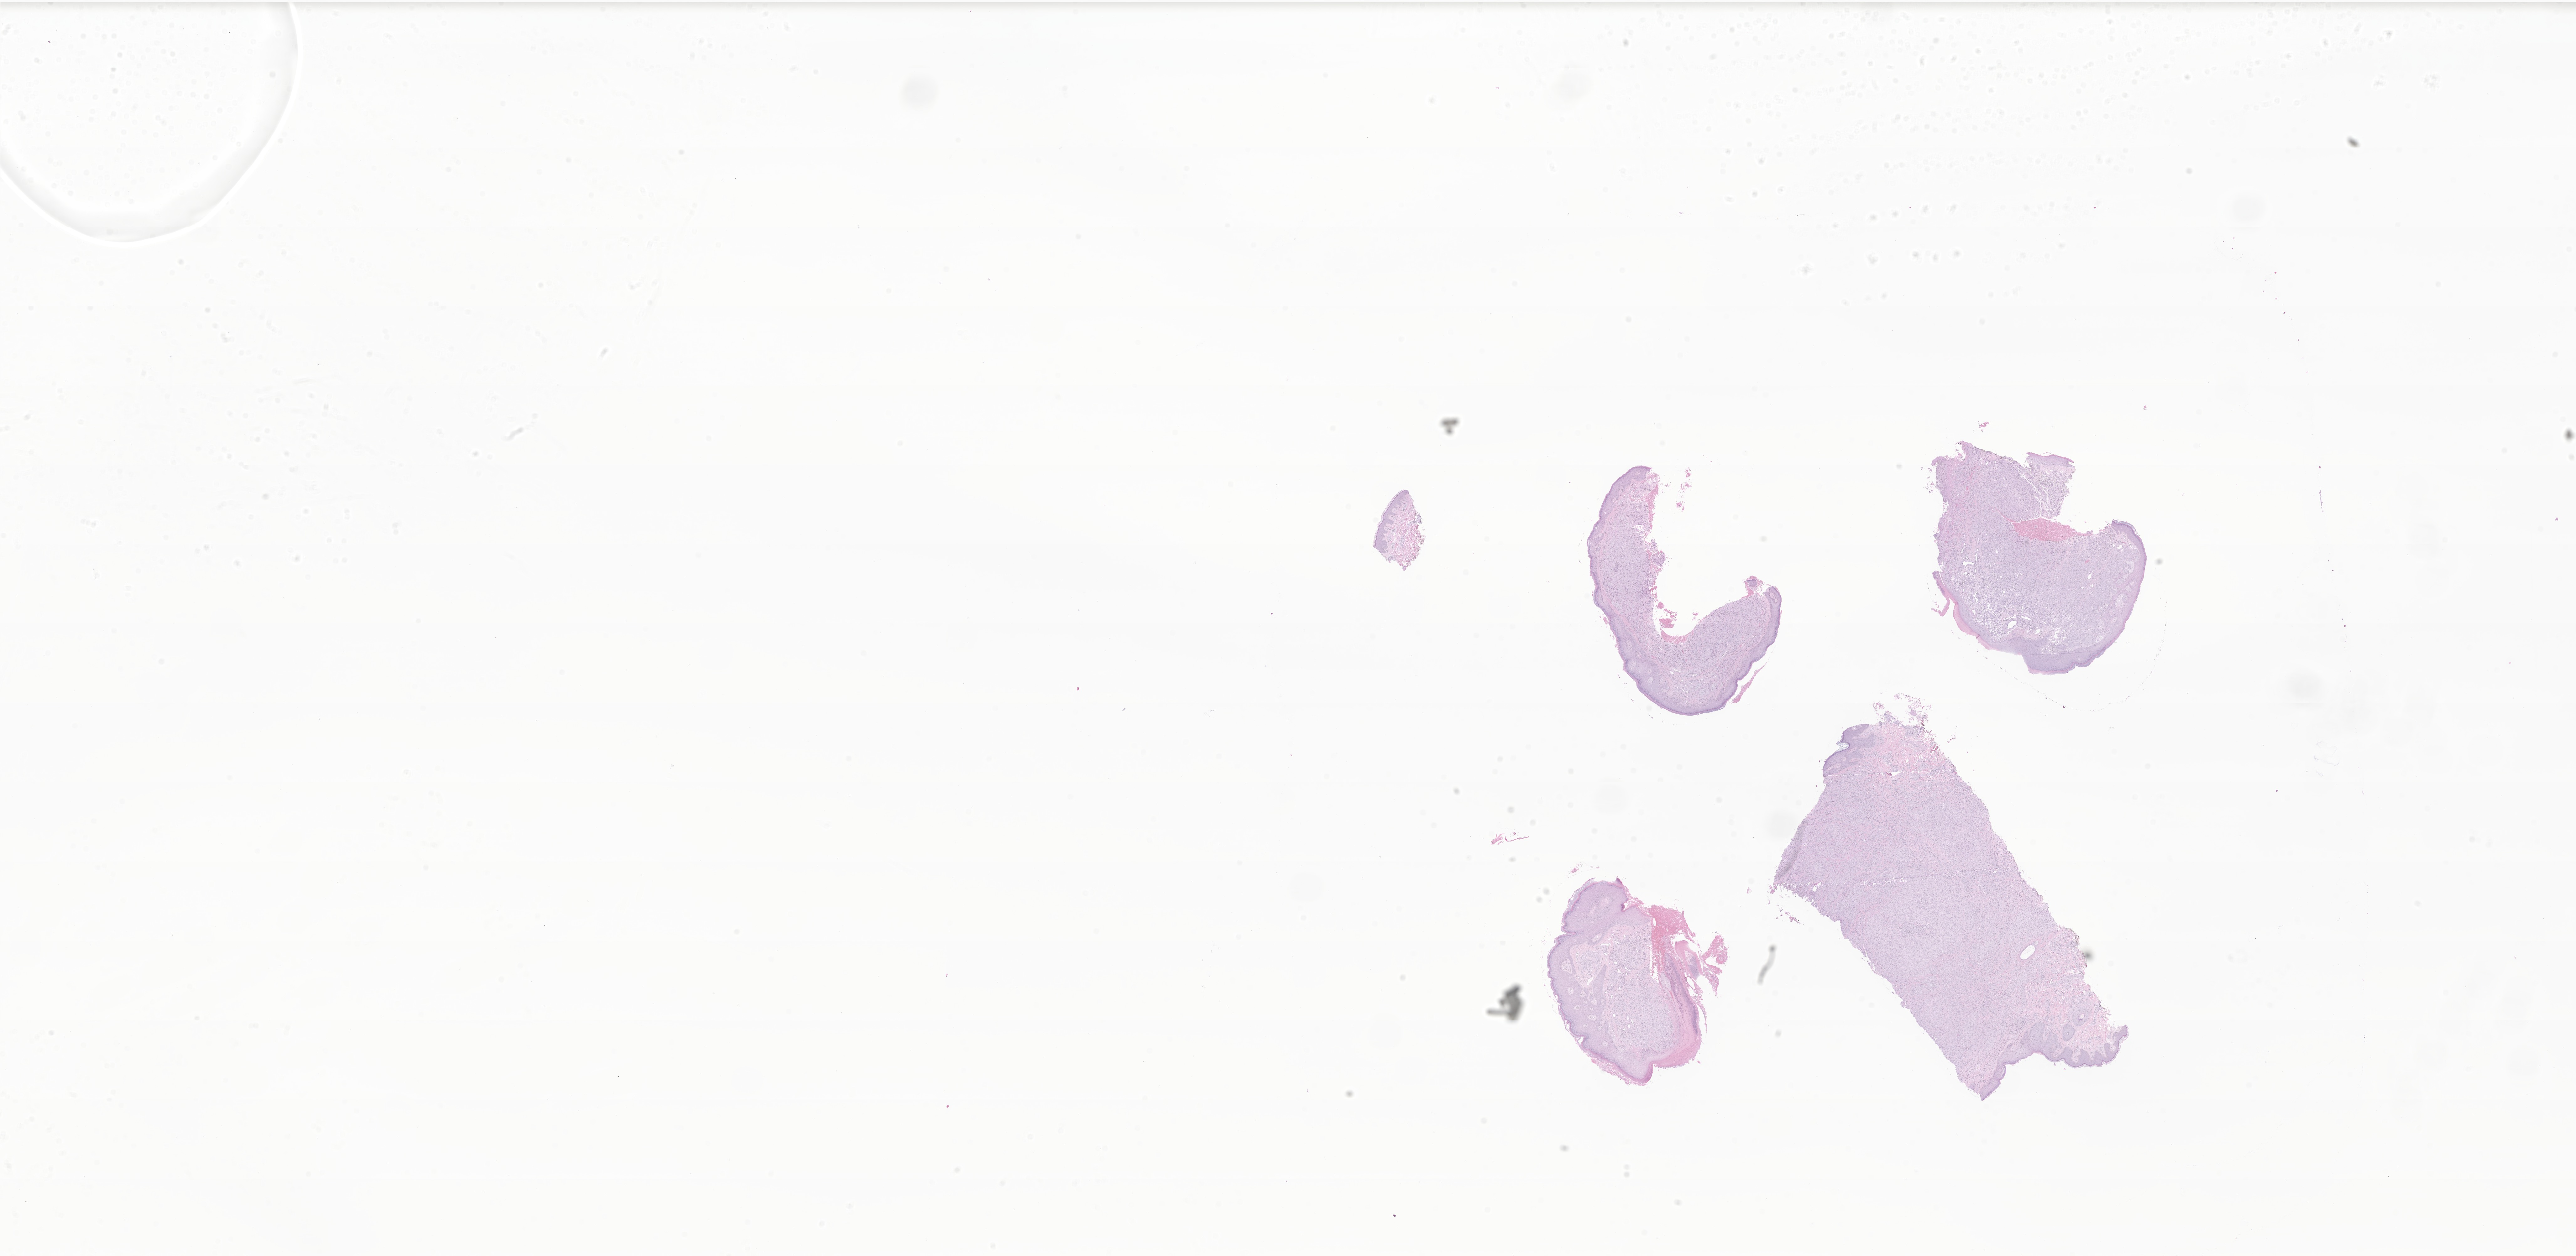
Hematoxylin and eosin (H&E) whole-slide image of tumor tissue from the skin of trunk — whole scanned area (about 34.7 x 16.9 mm) shown as a low-resolution overview; formalin-fixed paraffin-embedded section. Patient male; age 60 months (5 years).
Recorded diagnosis: Malignant melanoma, NOS.